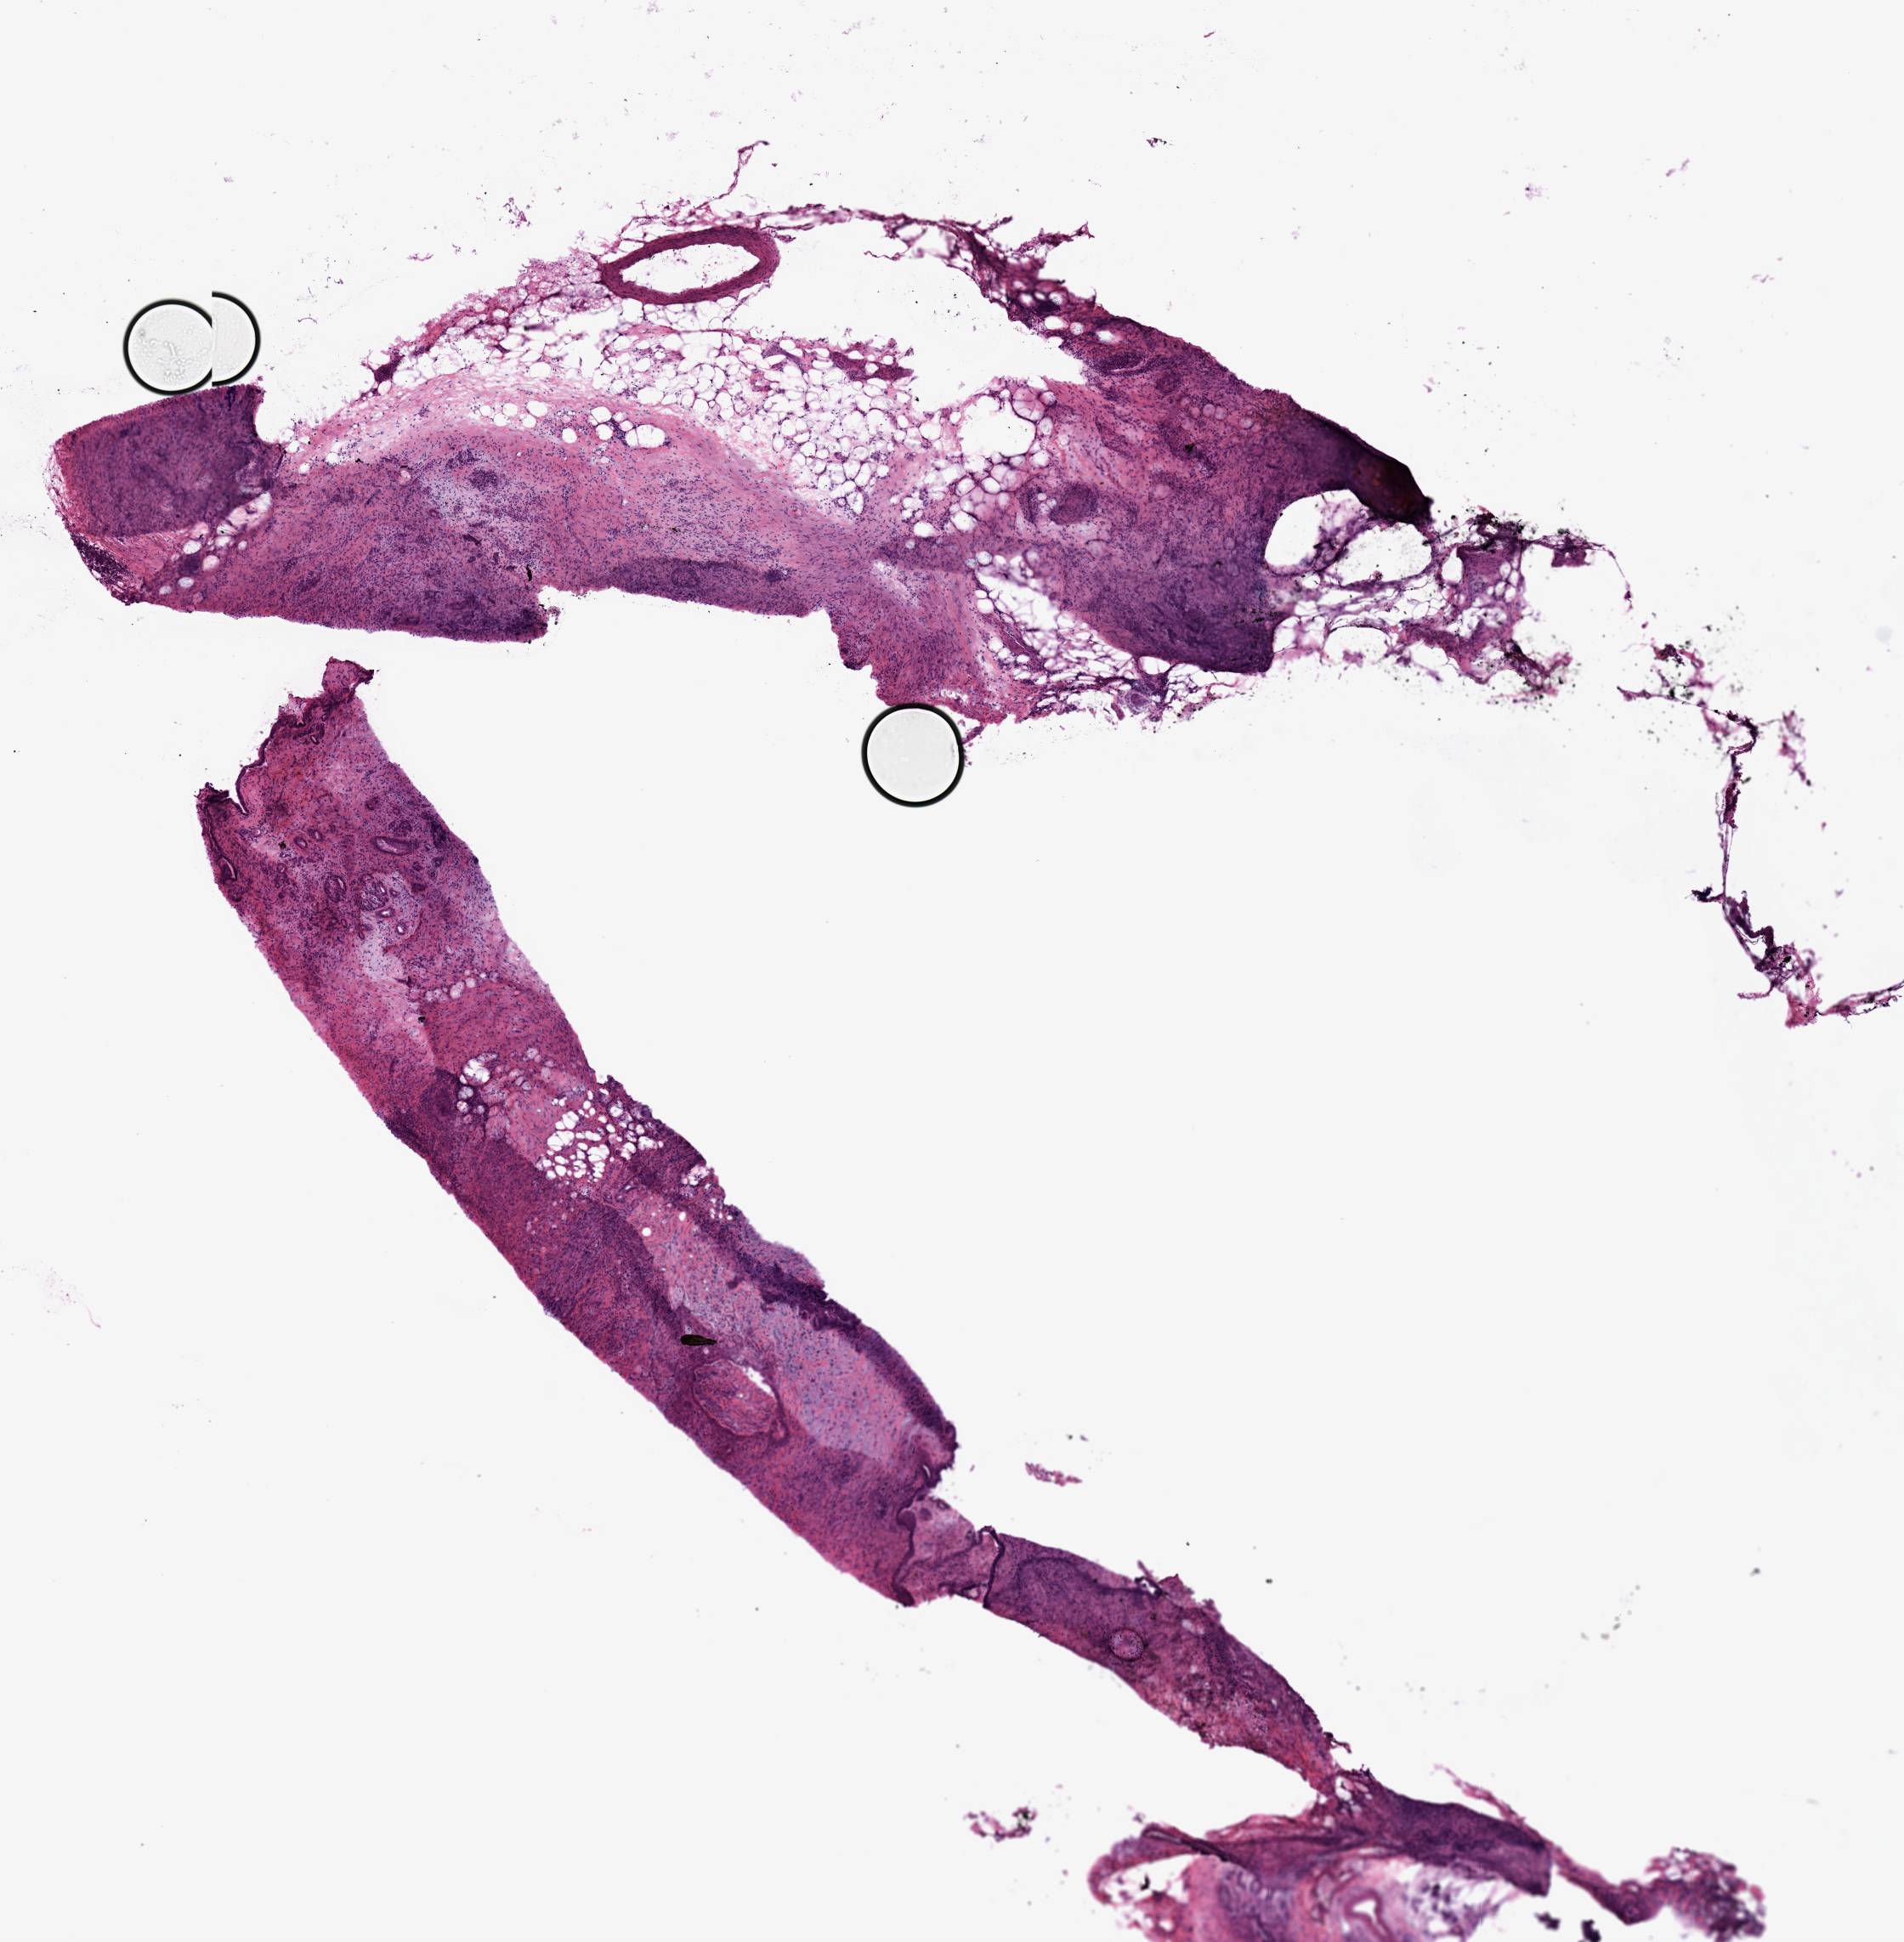
H&E whole-slide image, whole scanned area (about 8.9 x 9.0 mm, acquisition: 20x scan) shown as a low-resolution overview, frozen section from the top of the tissue portion, pancreas, primary tumour sample. Male patient; age at initial diagnosis 65 years.
Pathologic diagnosis: Infiltrating duct carcinoma, NOS.